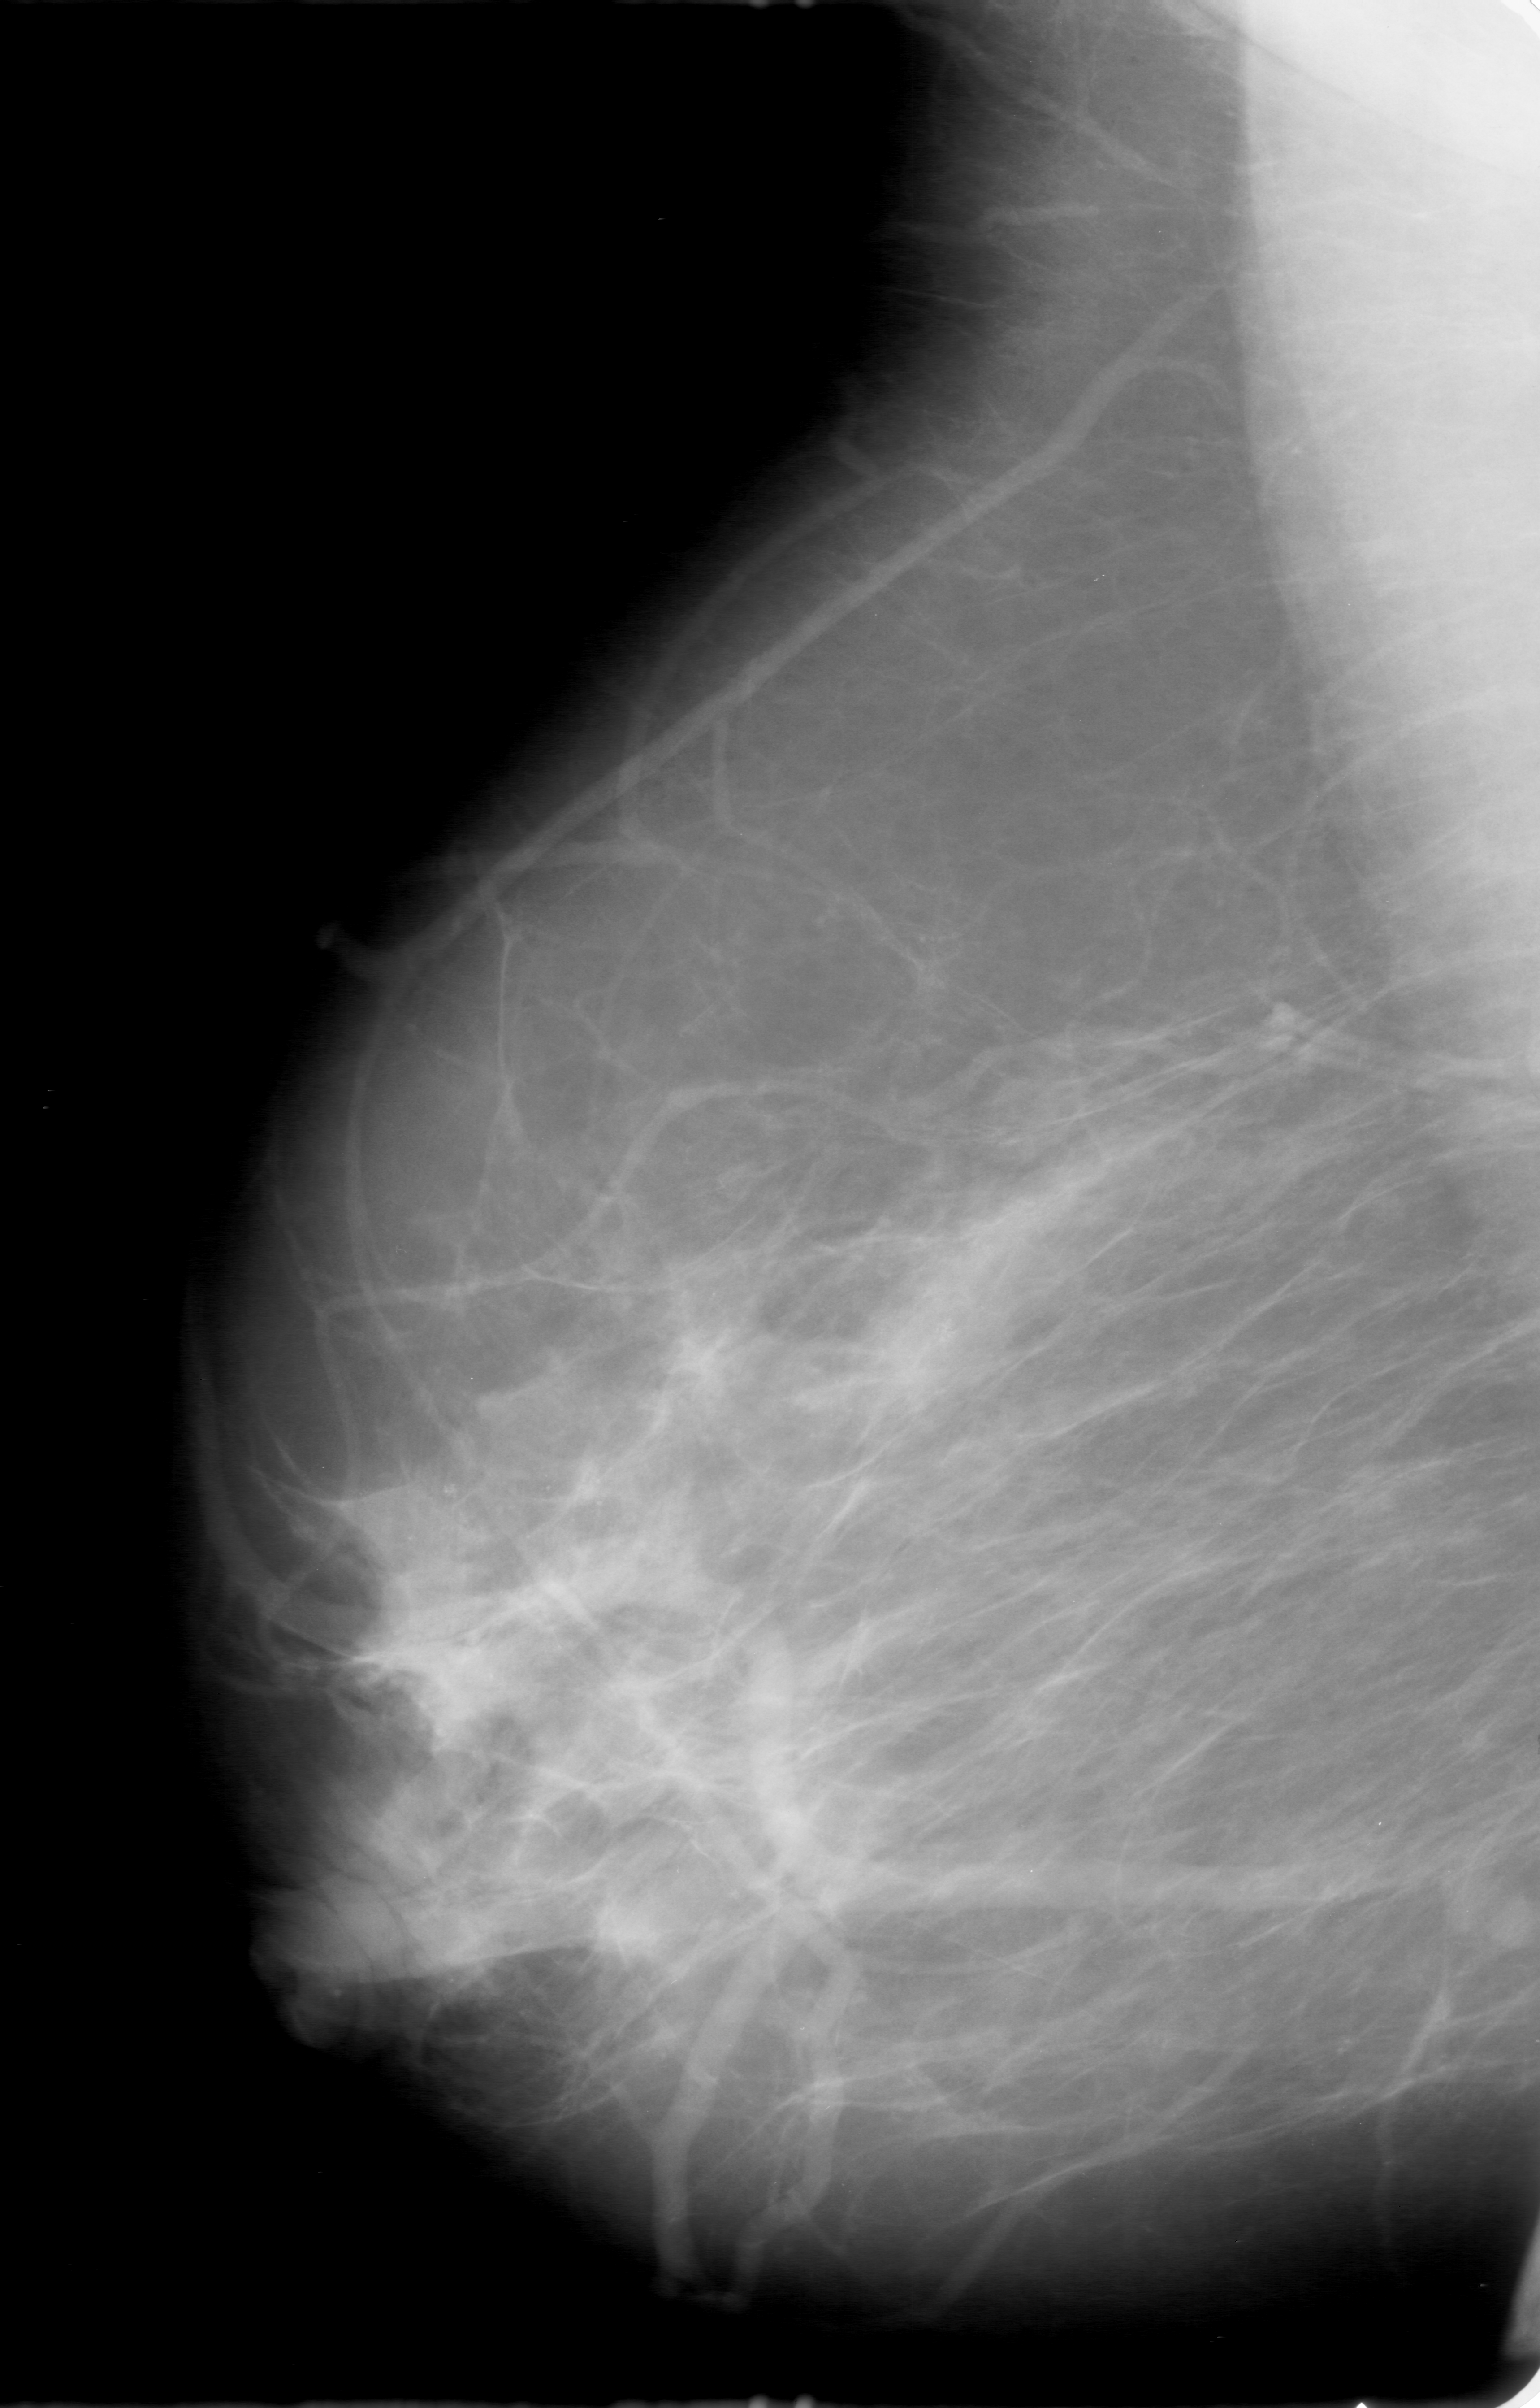
Digitized screen-film mammogram; right breast; MLO view; 1540 × 2408 image matrix.
Expert-marked regions of interest on this image (one box per marked abnormality):
- calcifications, morphology amorphous, distribution segmental; BI-RADS assessment category 0 (incomplete: needs additional imaging); pathology result (as recorded, not read from the image): malignant: bounding box [x1, y1, x2, y2] px = [268, 1041, 1191, 1824]